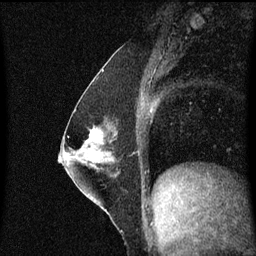
Breast MRI (dynamic contrast-enhanced), one sagittal slice; position 26 of 60 along the scan axis; dynamic contrast-enhanced series, image 2 of 3 at this slice position (ordered by acquisition); 1.5 T; TE 4.2 ms, TR 8.4 ms; 2 mm slice thickness; 256 × 256 image matrix, field of view 200 × 200 mm. Patient: female, 52 years. From the clinical record (not read from this slice): setting: breast cancer imaged before/during neoadjuvant chemotherapy; receptor status: HER2-positive.
Annotated regions visible in this slice (semi-automatically segmented with operator editing):
- analysis volume of interest (the breast-tissue region the enhancement analysis was run in; not a lesion): bounding box <71,118,122,187> (left, top, right, bottom; pixels)
- tumour enhancement mask (voxels above the 70 % enhancement threshold inside the analysis volume of interest): <88,130,100,141>